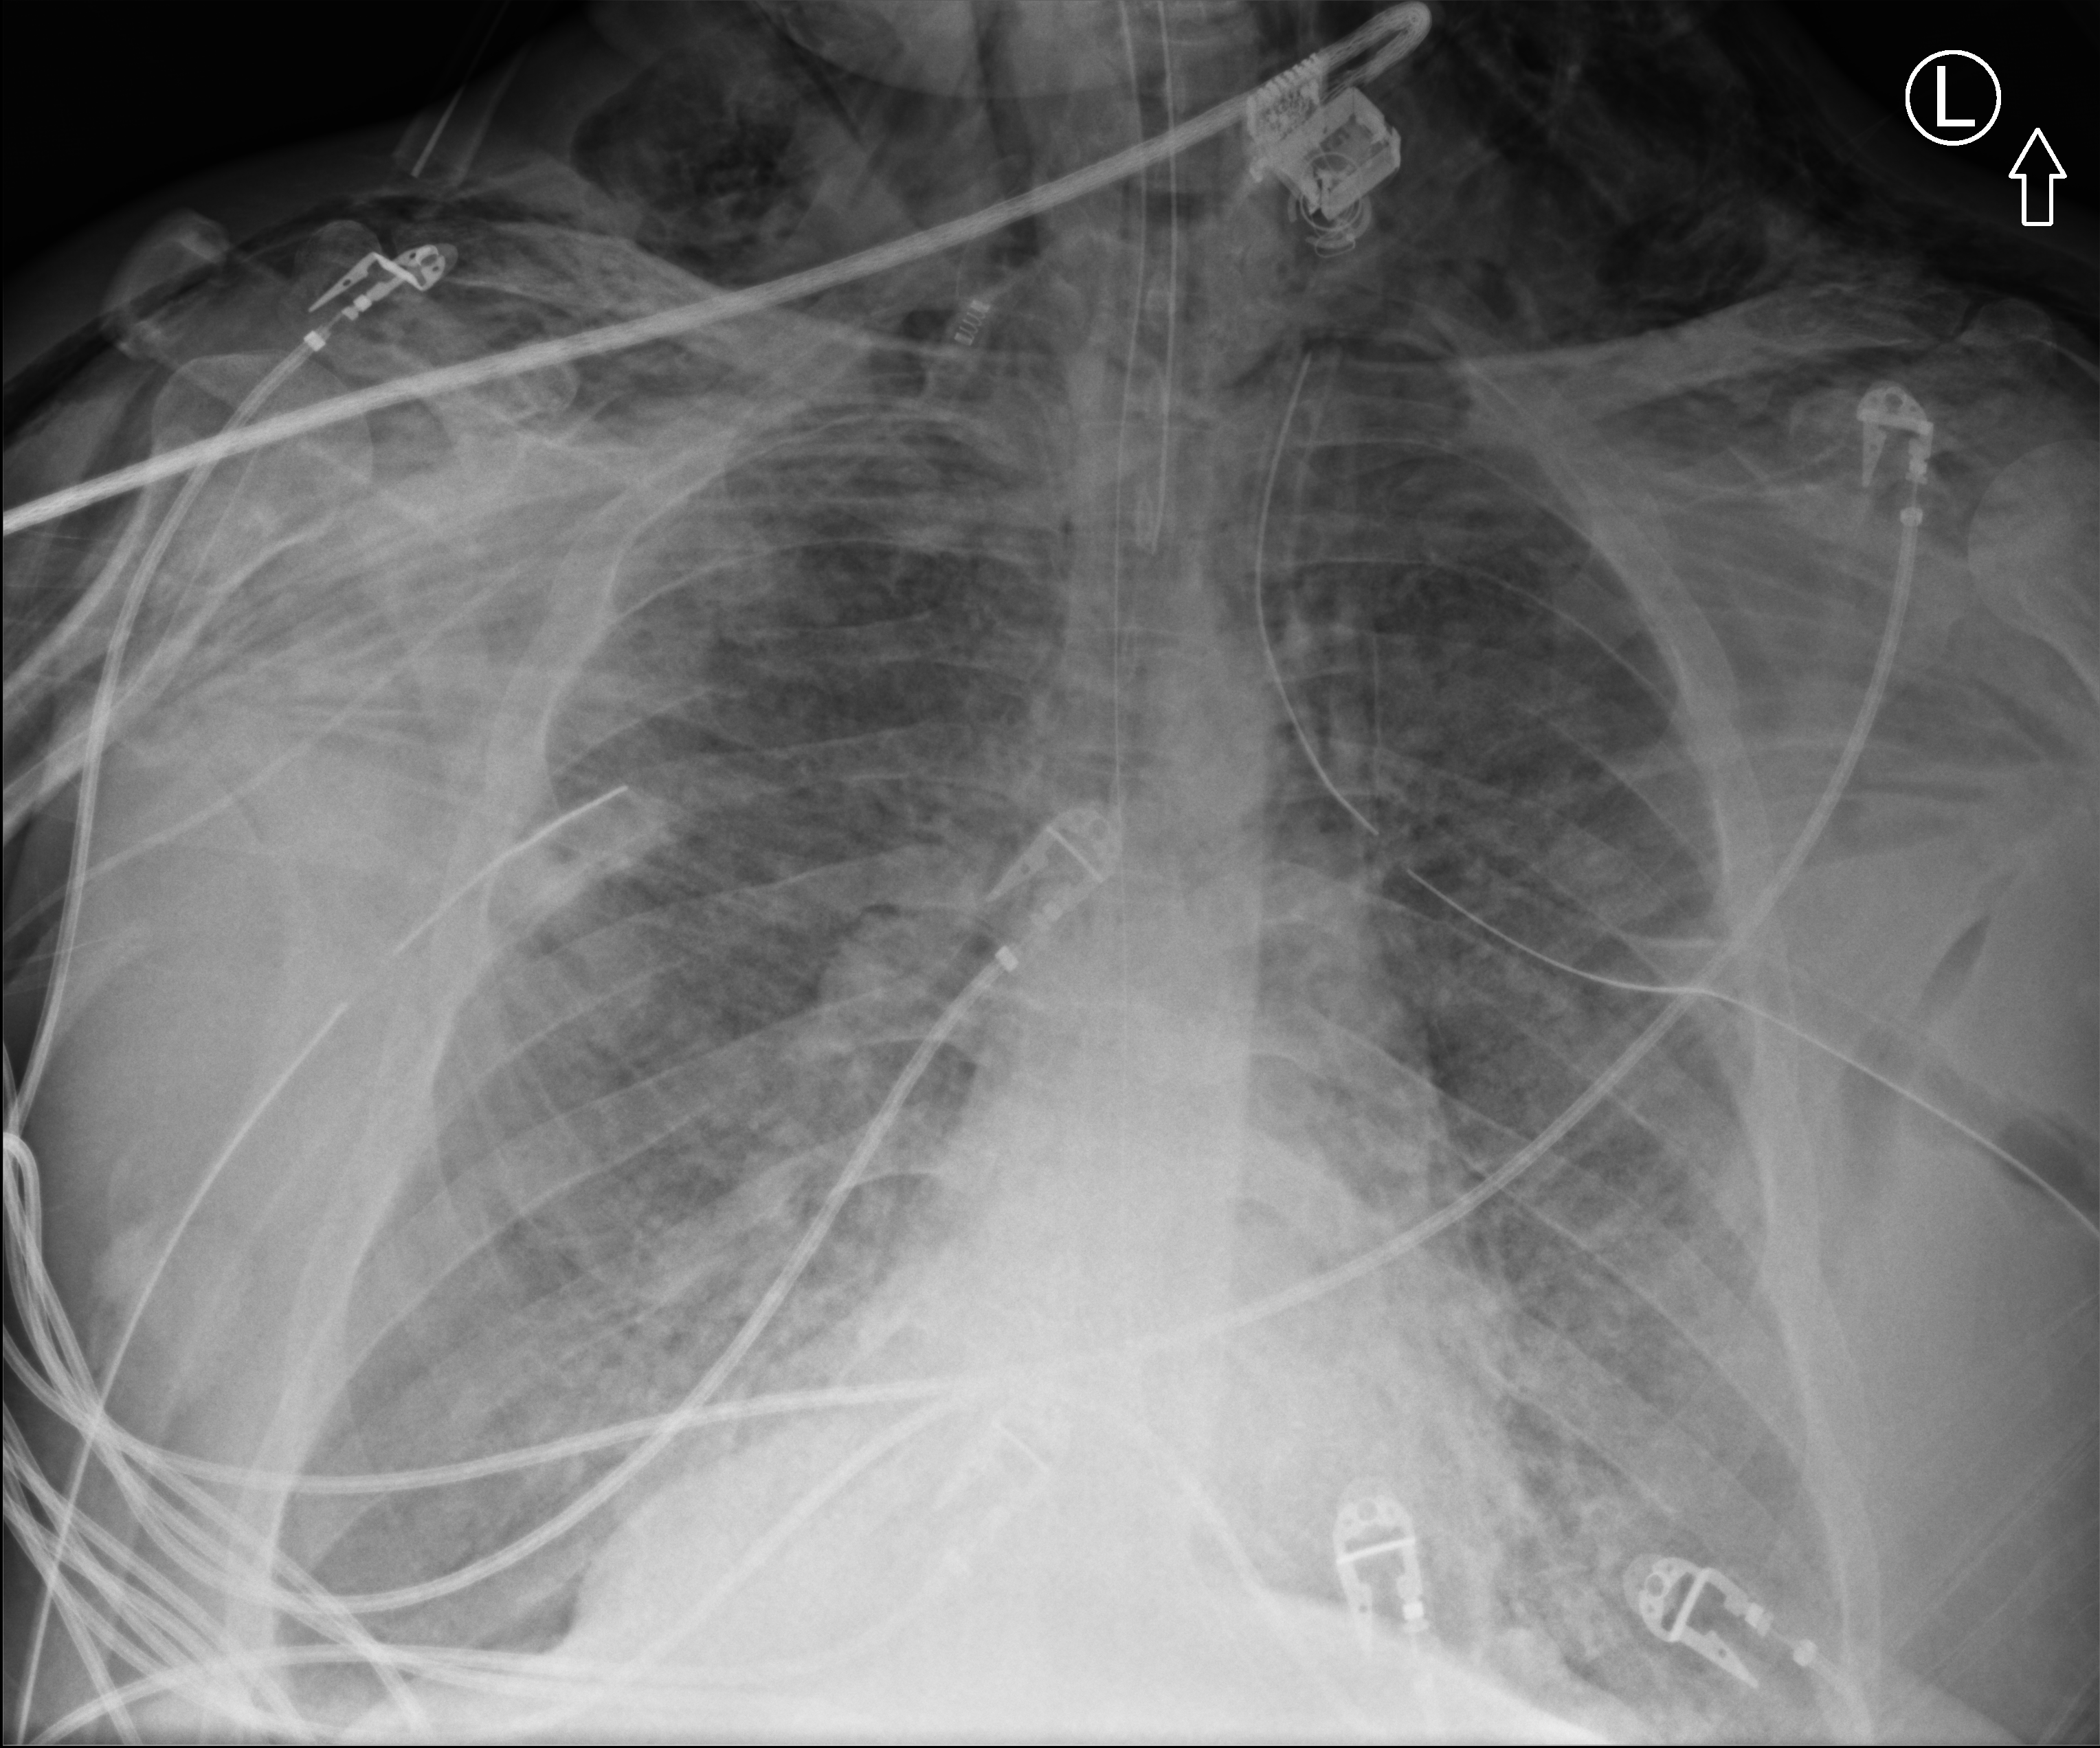
Portable chest radiograph; anteroposterior (AP) projection. Patient hospitalised with COVID-19, aged 18–59 years.
Hospital-stay facts (about this admission, not read from this image; timing relative to this image not recorded): diabetes (admission record): no.